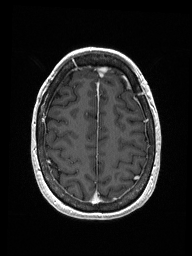
Brain MRI from a brain-tumour surgery series, one axial slice. Slice 44 of 192 in the series (ordered by position). T1-weighted post-contrast. 1 mm slice thickness. 192 × 256 image matrix, field of view 187 × 250 mm. Case-level facts recorded for this patient, not image findings: histopathology: Metastastic Carcinoma from Breast primary; tumour location: Right Frontal.
Structures marked on this image (manually delineated by an expert):
- previous resection cavity: box from (x=99, y=67) to (x=108, y=77) px